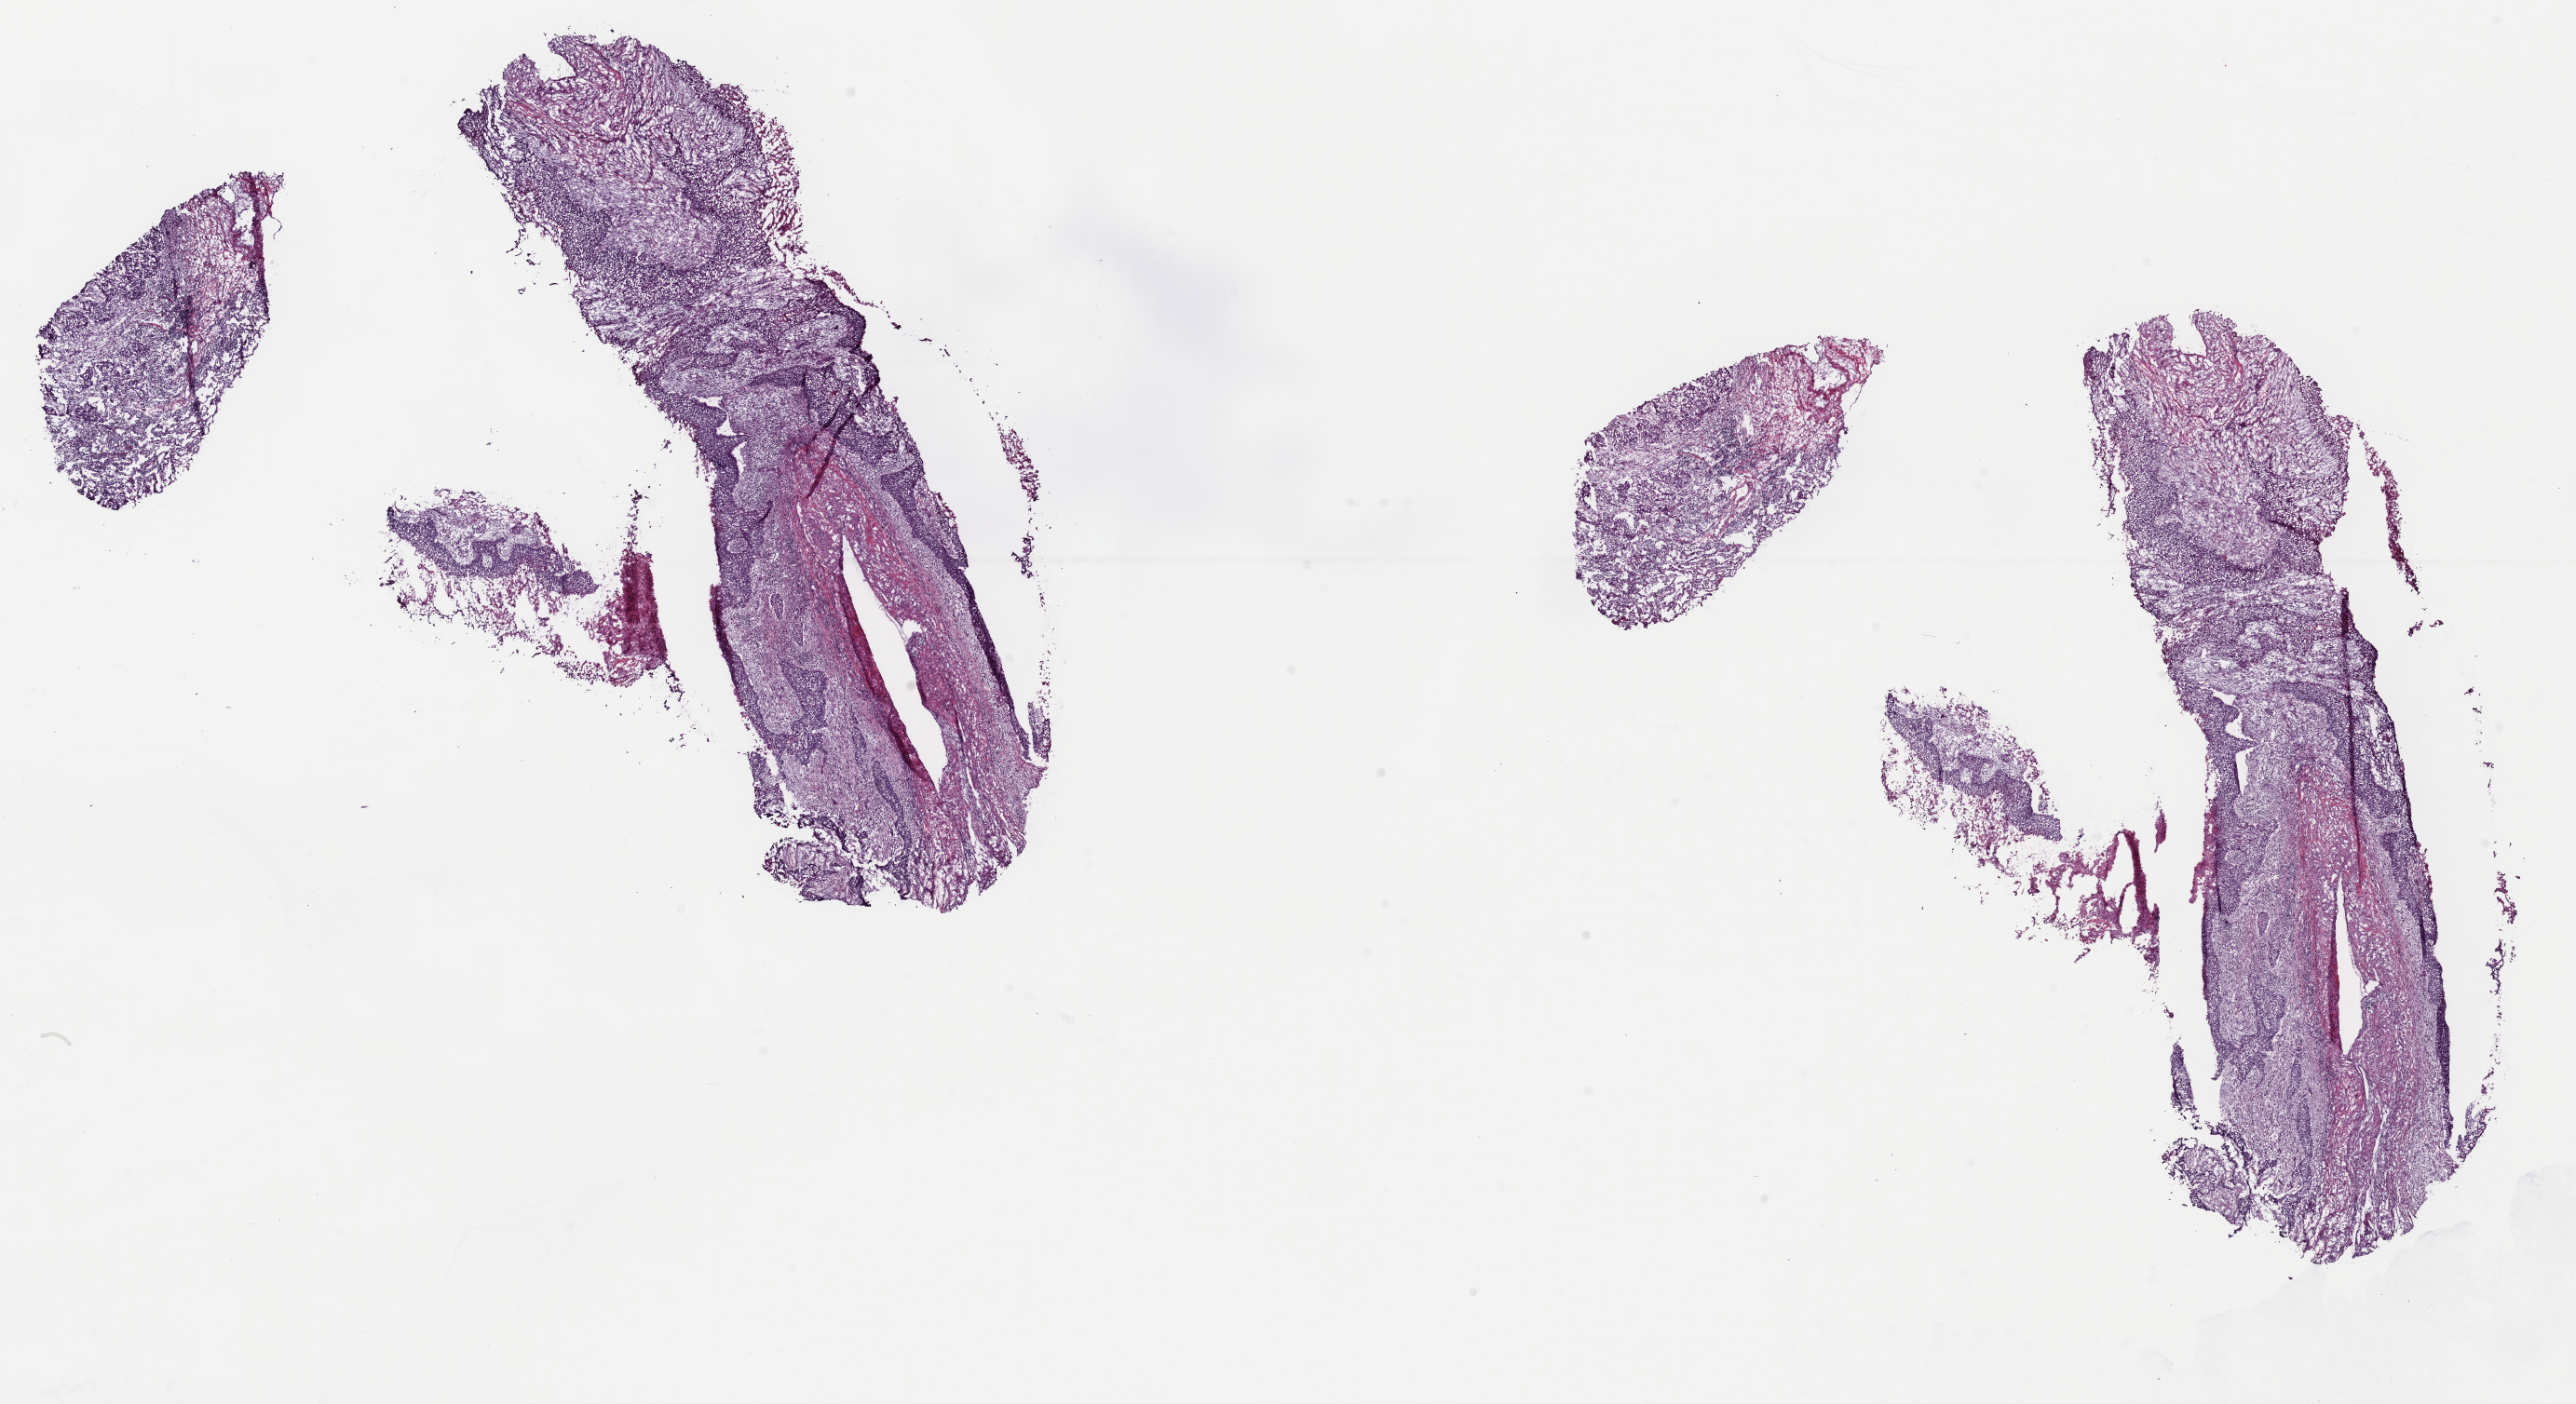
Whole-slide histology image, H&E-stained — whole scanned area (about 21.9 x 11.9 mm) shown as a low-resolution overview, frozen section from the top of the tissue portion, sample: primary tumour, lung. Patient: male, age at initial diagnosis 77 years. Composition of this section per pathologist review: tumour cells 40%, tumour nuclei 60%, normal cells 30%, stromal cells 20%, necrosis 10%. Infiltration values recorded for this section: lymphocyte infiltration 70%, monocyte infiltration 10%, neutrophil infiltration 5%.
• TNM: T1b N0 M0
• AJCC pathologic stage: IA
• laterality: right
• pathologic diagnosis: Squamous cell carcinoma, NOS (lower lobe, lung)